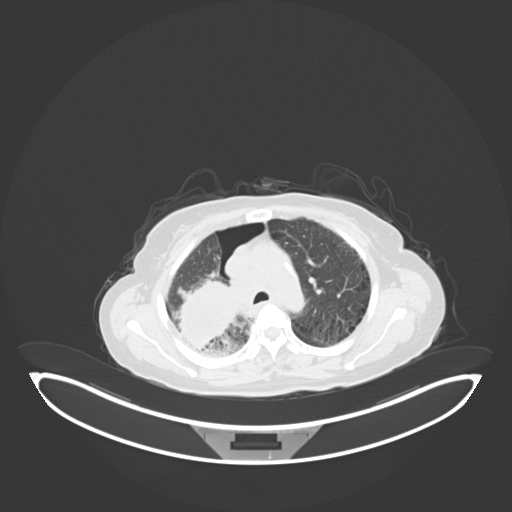
Chest CT, one axial slice. Position 43 of 69 along the scan axis. Reconstruction kernel B30f. 120 kVp. Lung window (W 1500 / L -600 HU). 512 × 512 image matrix, field of view 500 × 500 mm. Female patient, age 64 years. Case-level facts recorded for this patient, not image findings: clinical TNM (as recorded): T3 N3 M0.
Outlined on this slice (rectangle marked by the reading radiologist):
- lung tumour (recorded histology: squamous cell carcinoma): bounding box [x1, y1, x2, y2] px = [171, 276, 239, 352]